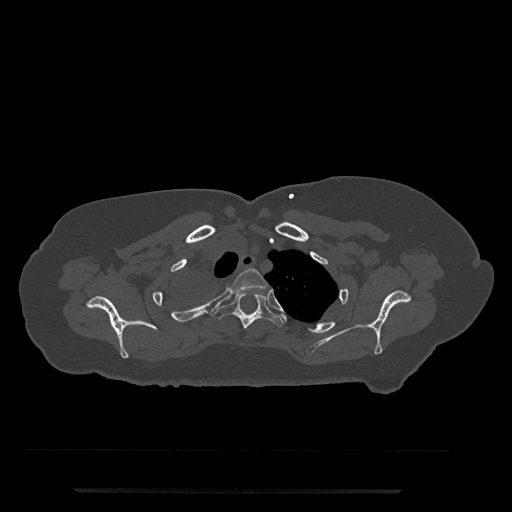
CT including the spine, one axial slice. Slice 644 of 797 in the series (ordered by position). Reconstruction kernel Br40s/3. 120 kVp. Bone window (W 1800 / L 400 HU). 0.5 mm slice thickness. 512 × 512 image matrix. Patient: female, 51 years. From the clinical record (not read from this slice): primary cancer: neuro; vertebrae with lytic lesions (as recorded): T8.
Outlined on this slice (semi-automatic segmentation, software-assisted and operator-edited):
- T2 vertebra: bounding box <228,268,268,293> (left, top, right, bottom; pixels)
- T3 vertebra: <212,291,285,329>